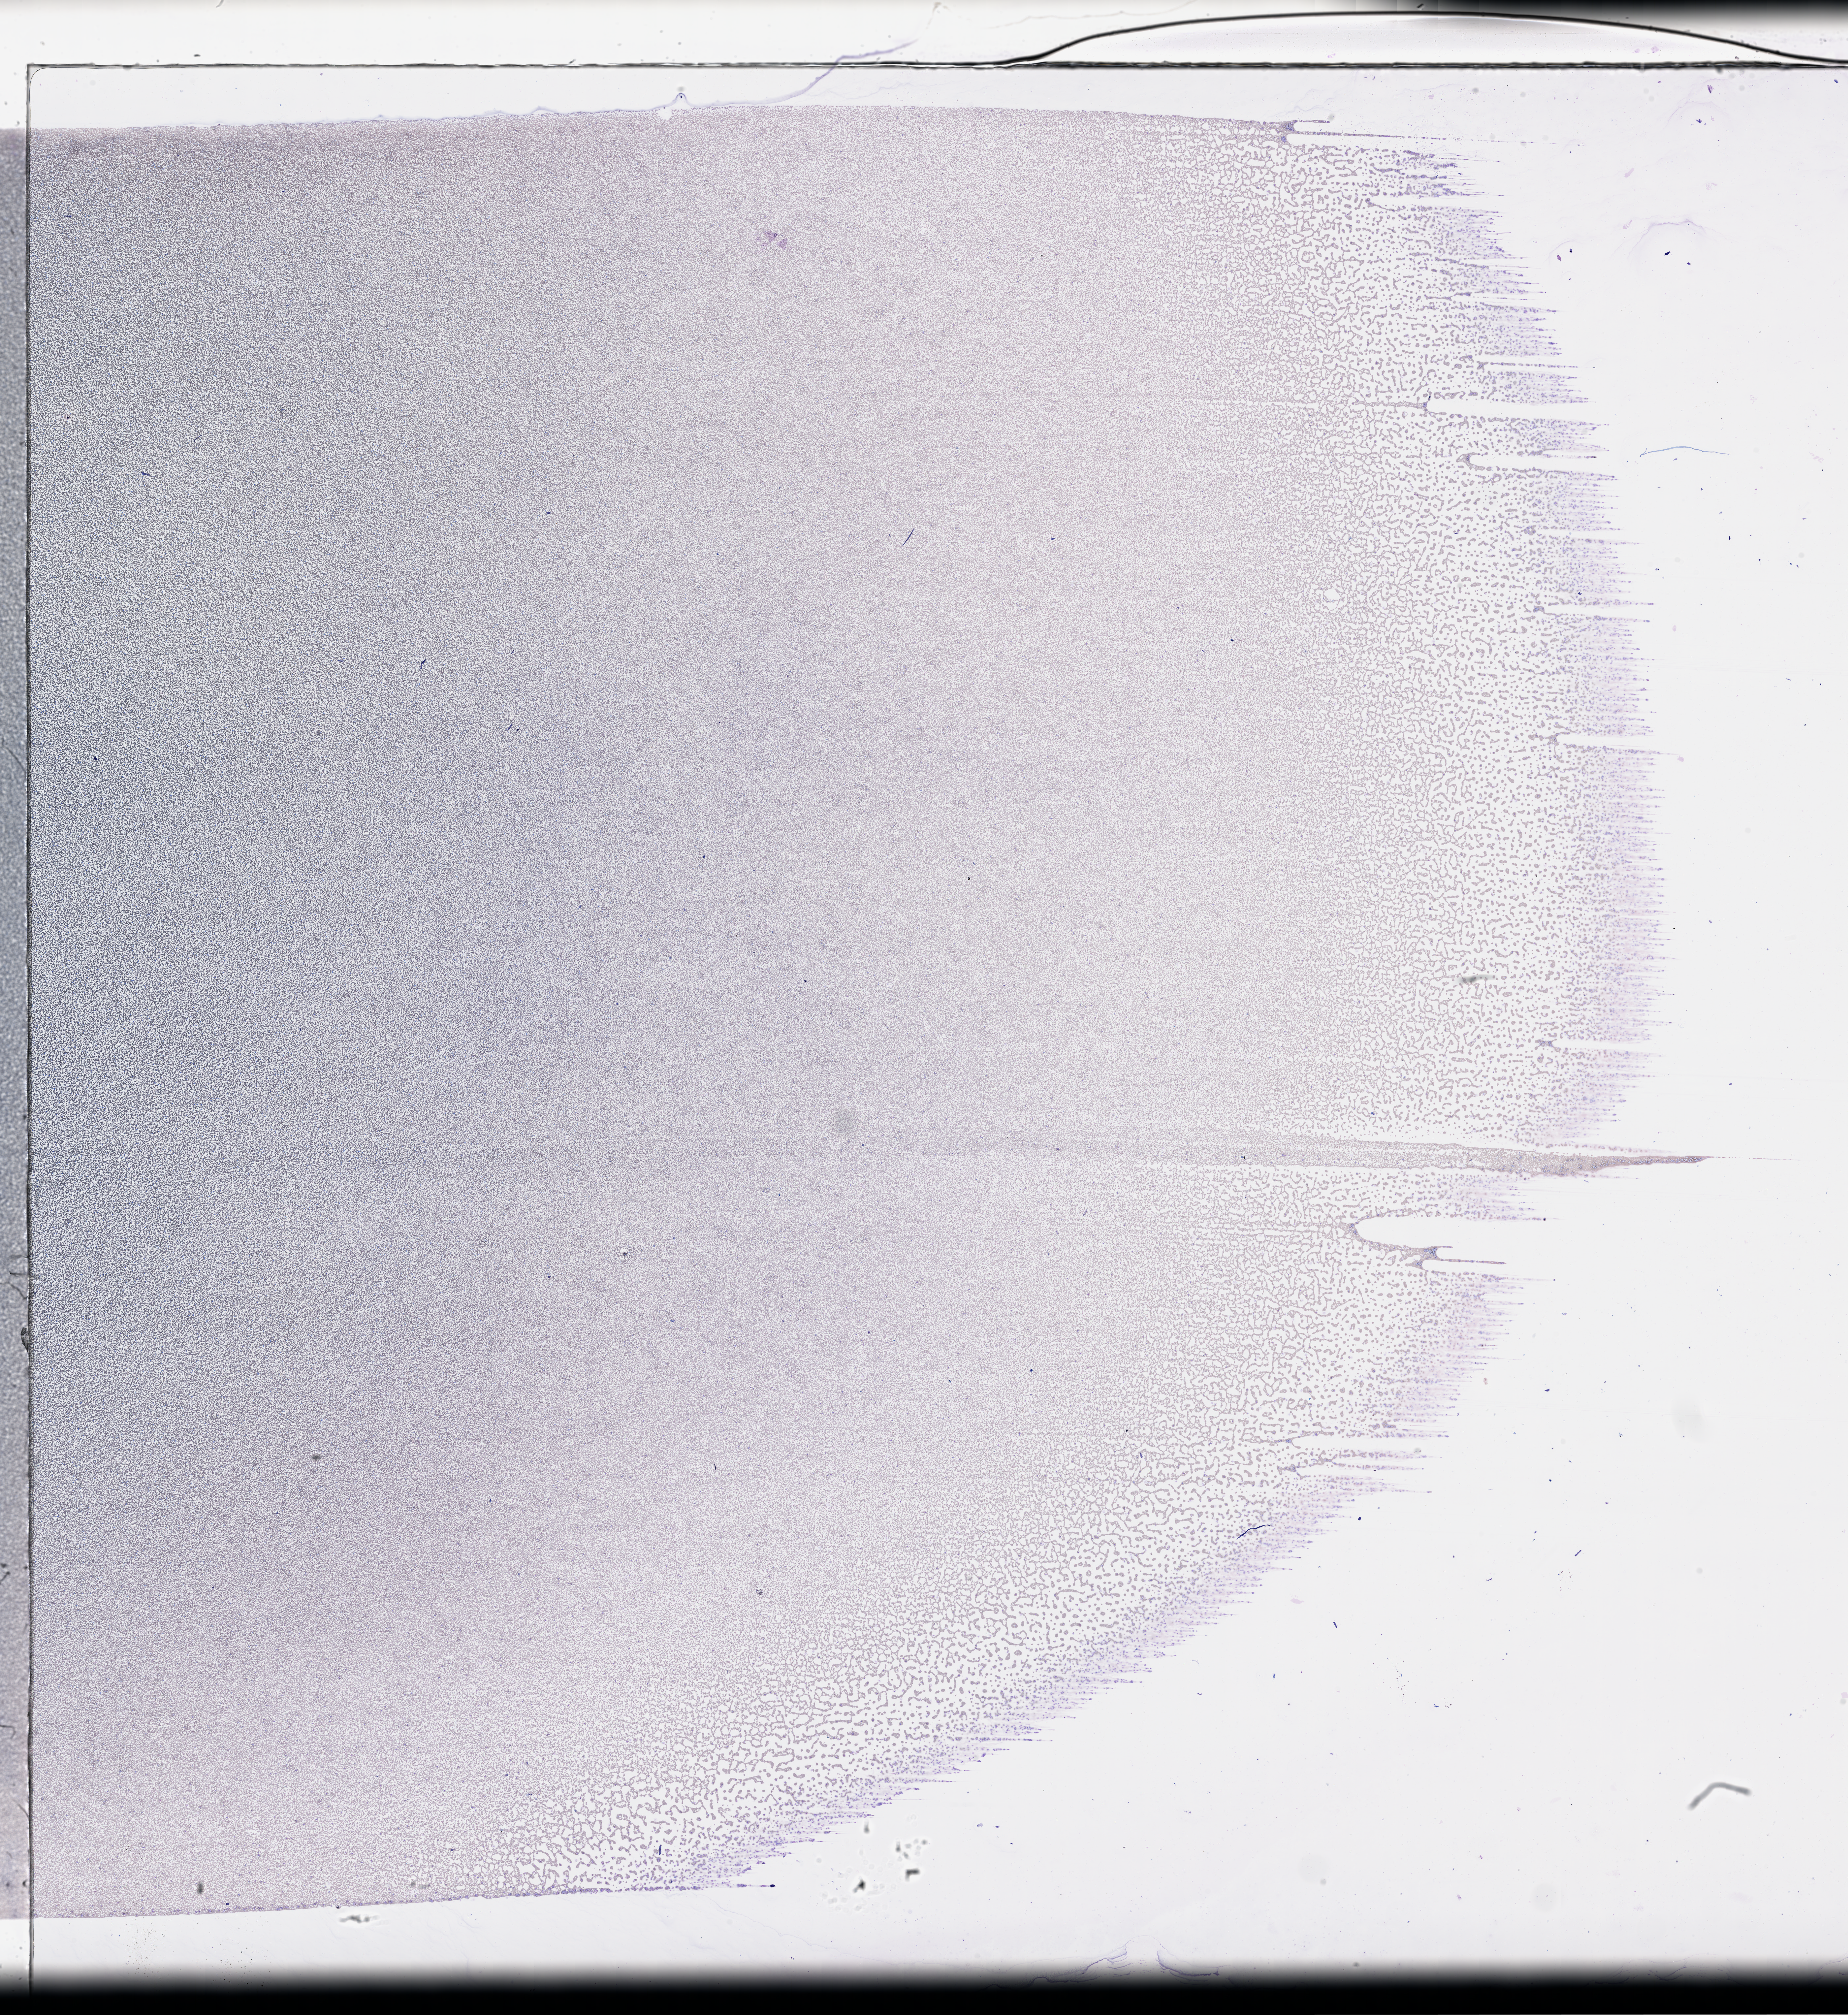
Hematoxylin and eosin (H&E) stained whole-slide image — shown as a low-resolution overview of the whole scanned area (about 22.6 x 24.7 mm), peripheral blood (leukaemic) sample. Patient: female, age 48 years.
- WHO classification: Acute myelomonocytic leukemia
- diagnosis: Acute Myeloid Leukemia
- FAB classification: M4